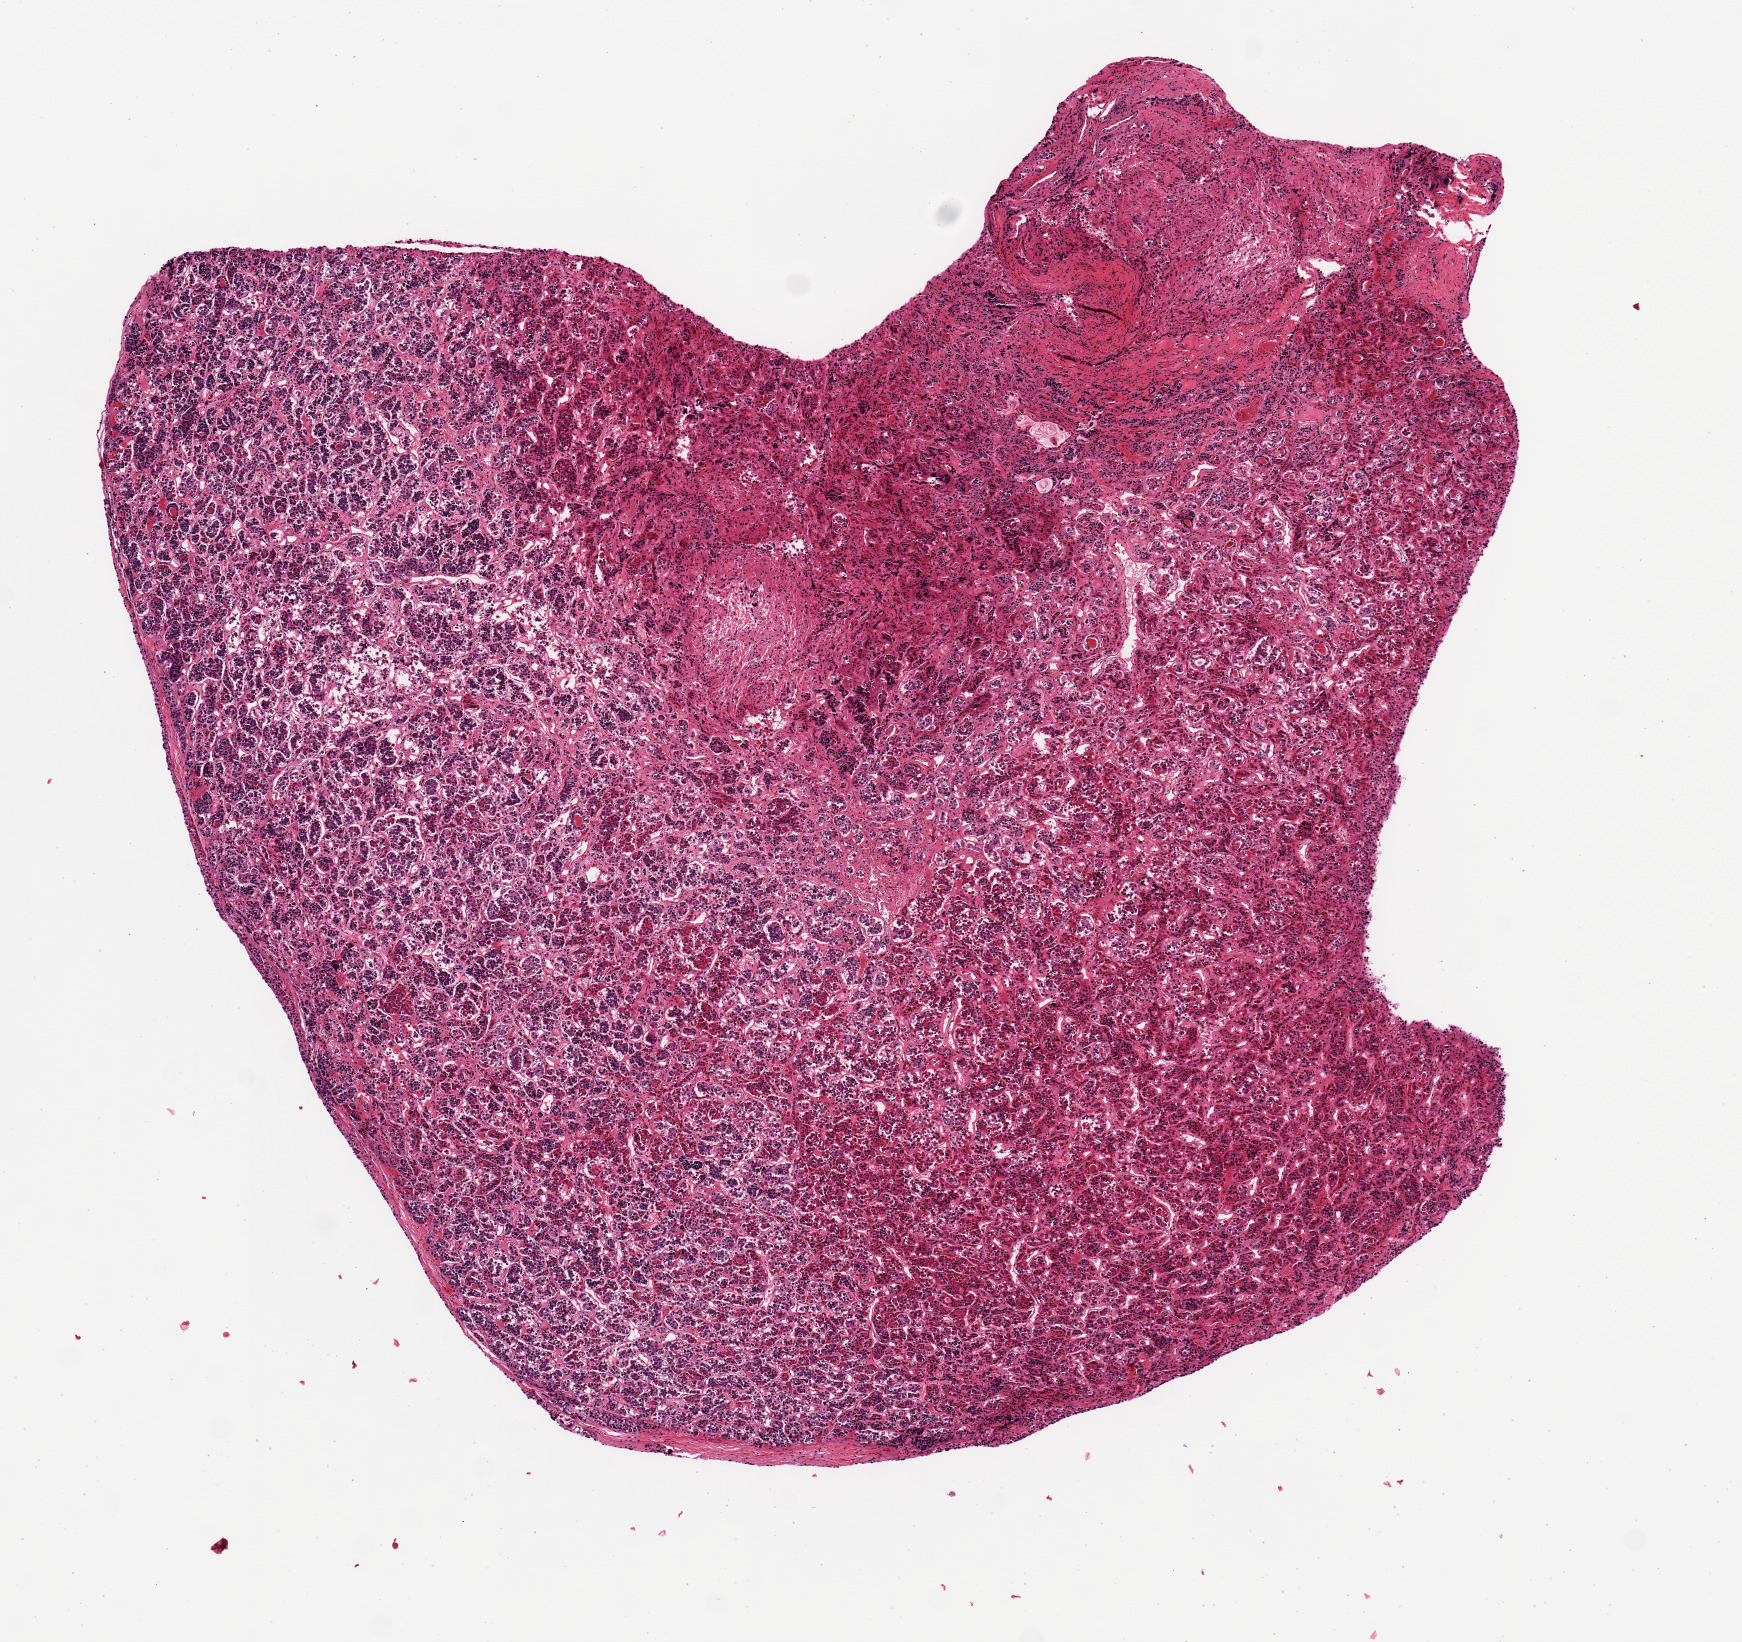
H&E whole-slide image, whole scanned area (about 6.9 x 6.5 mm) shown as a low-resolution overview; PAXgene-fixed paraffin-embedded (PFPE) section; sampled site (target tissue): pituitary; donor tissue sample. Male donor.
• review note (as recorded): 6.24x9mm